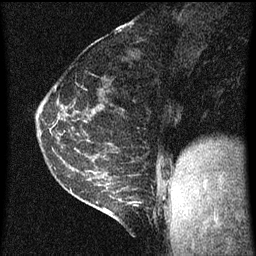
Breast MRI (dynamic contrast-enhanced), one sagittal slice; position 23 of 60 along the scan axis; dynamic contrast-enhanced series, image 2 of 3 at this slice position (ordered by acquisition); 1.5 T; TE 4.2 ms, TR 8 ms; 2 mm slice thickness; 256 × 256 image matrix. Female patient, age 35 years.
Outlined on this slice (semi-automatically segmented with operator editing):
- analysis volume of interest (the breast-tissue region the enhancement analysis was run in; not a lesion): bounding box (x1, y1, x2, y2) in pixels: (106, 182, 143, 223)
- tumour enhancement mask (voxels above the 70 % enhancement threshold inside the analysis volume of interest): (106, 202, 137, 215)